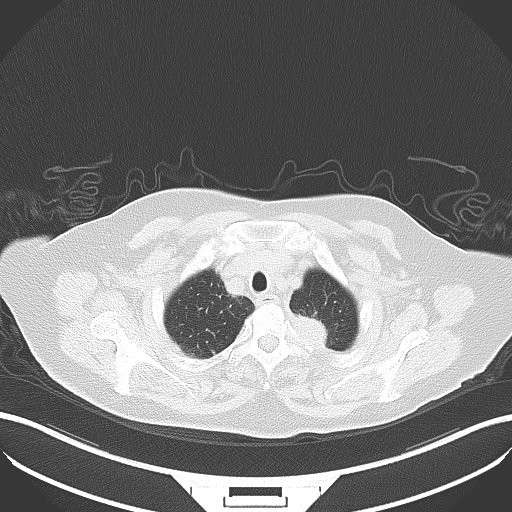
Chest CT, one axial slice; position 43 of 50 along the scan axis; reconstruction kernel B80f; 100 kVp; lung window (W 1500 / L -600 HU); 5 mm slice thickness; 512 × 512 image matrix, field of view 400 × 400 mm. Patient: female, 81 years. Case-level facts recorded for this patient, not image findings: clinical TNM (as recorded): T2a N0 M0.
Structures marked on this image (rectangle marked by the reading radiologist):
- lung tumour (recorded histology: adenocarcinoma): bounding box <293,309,331,350> (left, top, right, bottom; pixels)